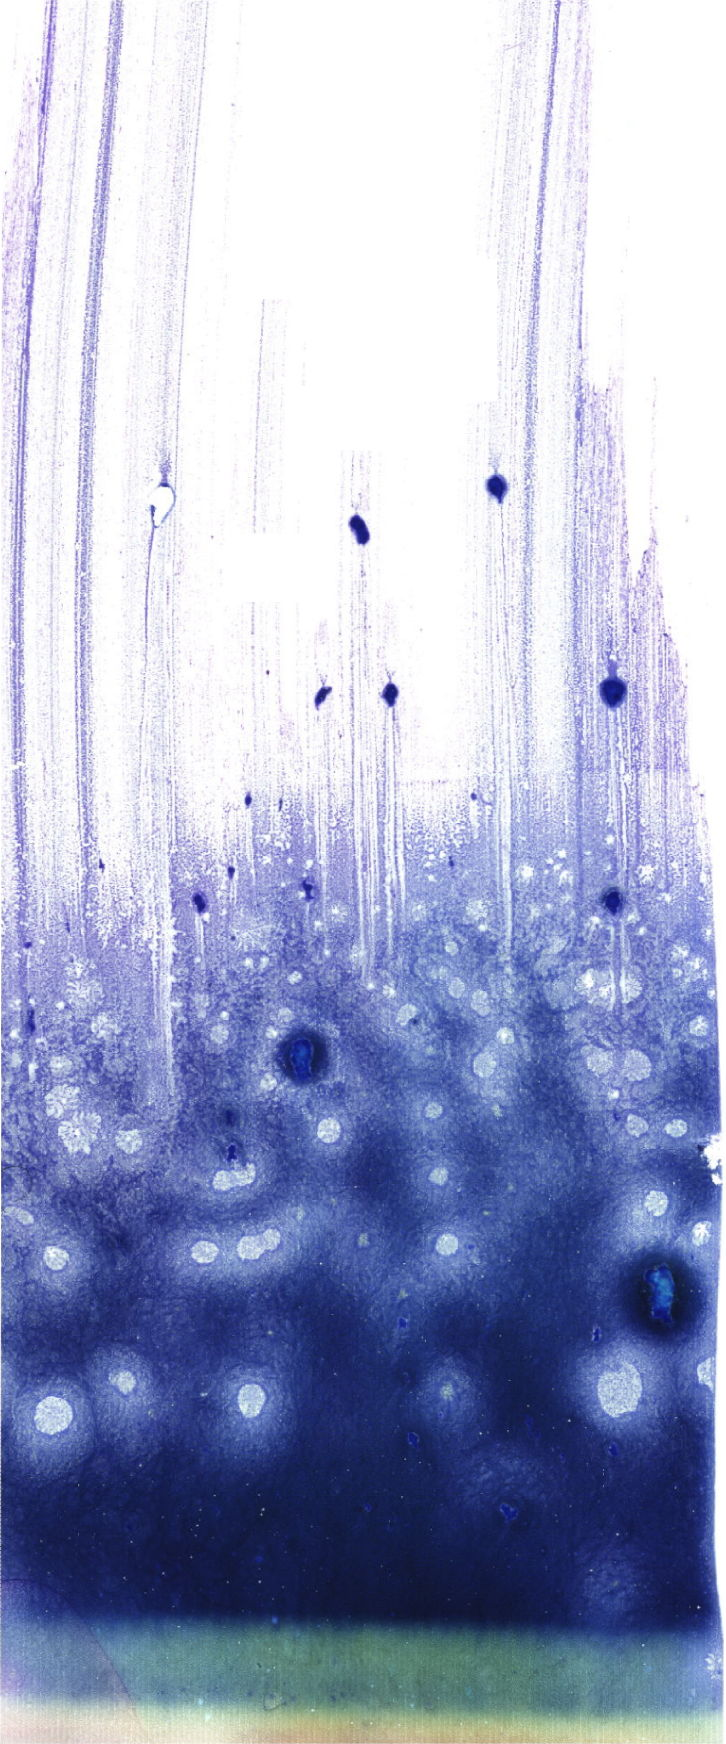
Bone marrow aspirate smear, May-Grünwald–Giemsa stain, whole-slide image — low-resolution overview of the scanned area, about 20.6 x 49.4 mm. Male patient.
Diagnosis: B Acute Lymphoblastic Leukemia.